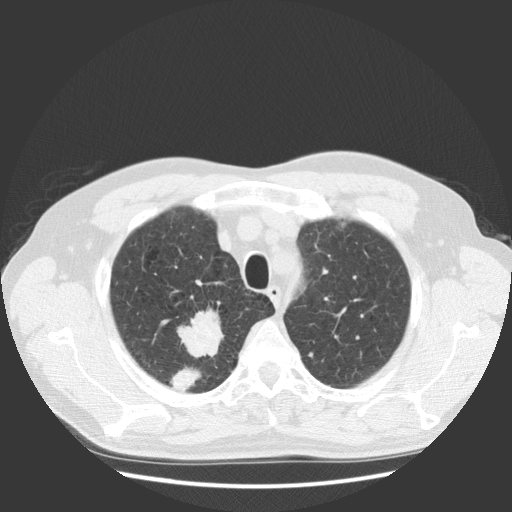
Low-dose screening chest CT, one axial slice. Position 104 of 131 along the scan axis. Reconstruction kernel STANDARD. 140 kVp. Lung window (W 1500 / L -600 HU). 2.5 mm slice thickness. 512 × 512 image matrix, field of view 369 × 369 mm.
Annotated regions visible in this slice (manually delineated by an expert):
- lesion 1 (tumor, upper lobe of right lung): bounding box (x1, y1, x2, y2) in pixels: (177, 308, 224, 358)
- lesion 2 (tumor, upper lobe of right lung): (171, 367, 201, 391)